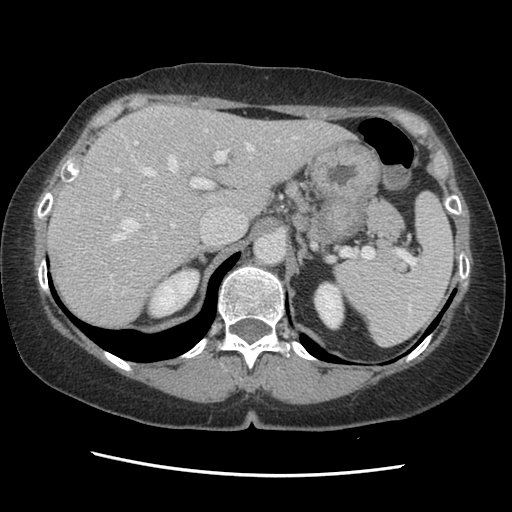
Contrast-enhanced abdominal CT, one axial slice; slice 96 of 141 in the series (ordered by position); 120 kVp; soft-tissue window (W 400 / L 40 HU); 2.5 mm slice thickness; 512 × 512 image matrix, field of view 330 × 330 mm. Female patient, age 61 years. Case-level facts recorded for this patient, not image findings: diagnosis: colorectal cancer liver metastases, imaged before liver resection; multiple liver metastases: no; largest metastasis: 2.4 cm.
Outlined on this slice (outlined manually by an expert reader):
- hepatic veins: bounding box <76,121,297,289> (left, top, right, bottom; pixels)
- liver: <48,106,348,329>
- planned liver remnant (the part of the liver to remain after resection): <48,106,348,329>
- portal vein (with intrahepatic branches): <110,141,228,277>